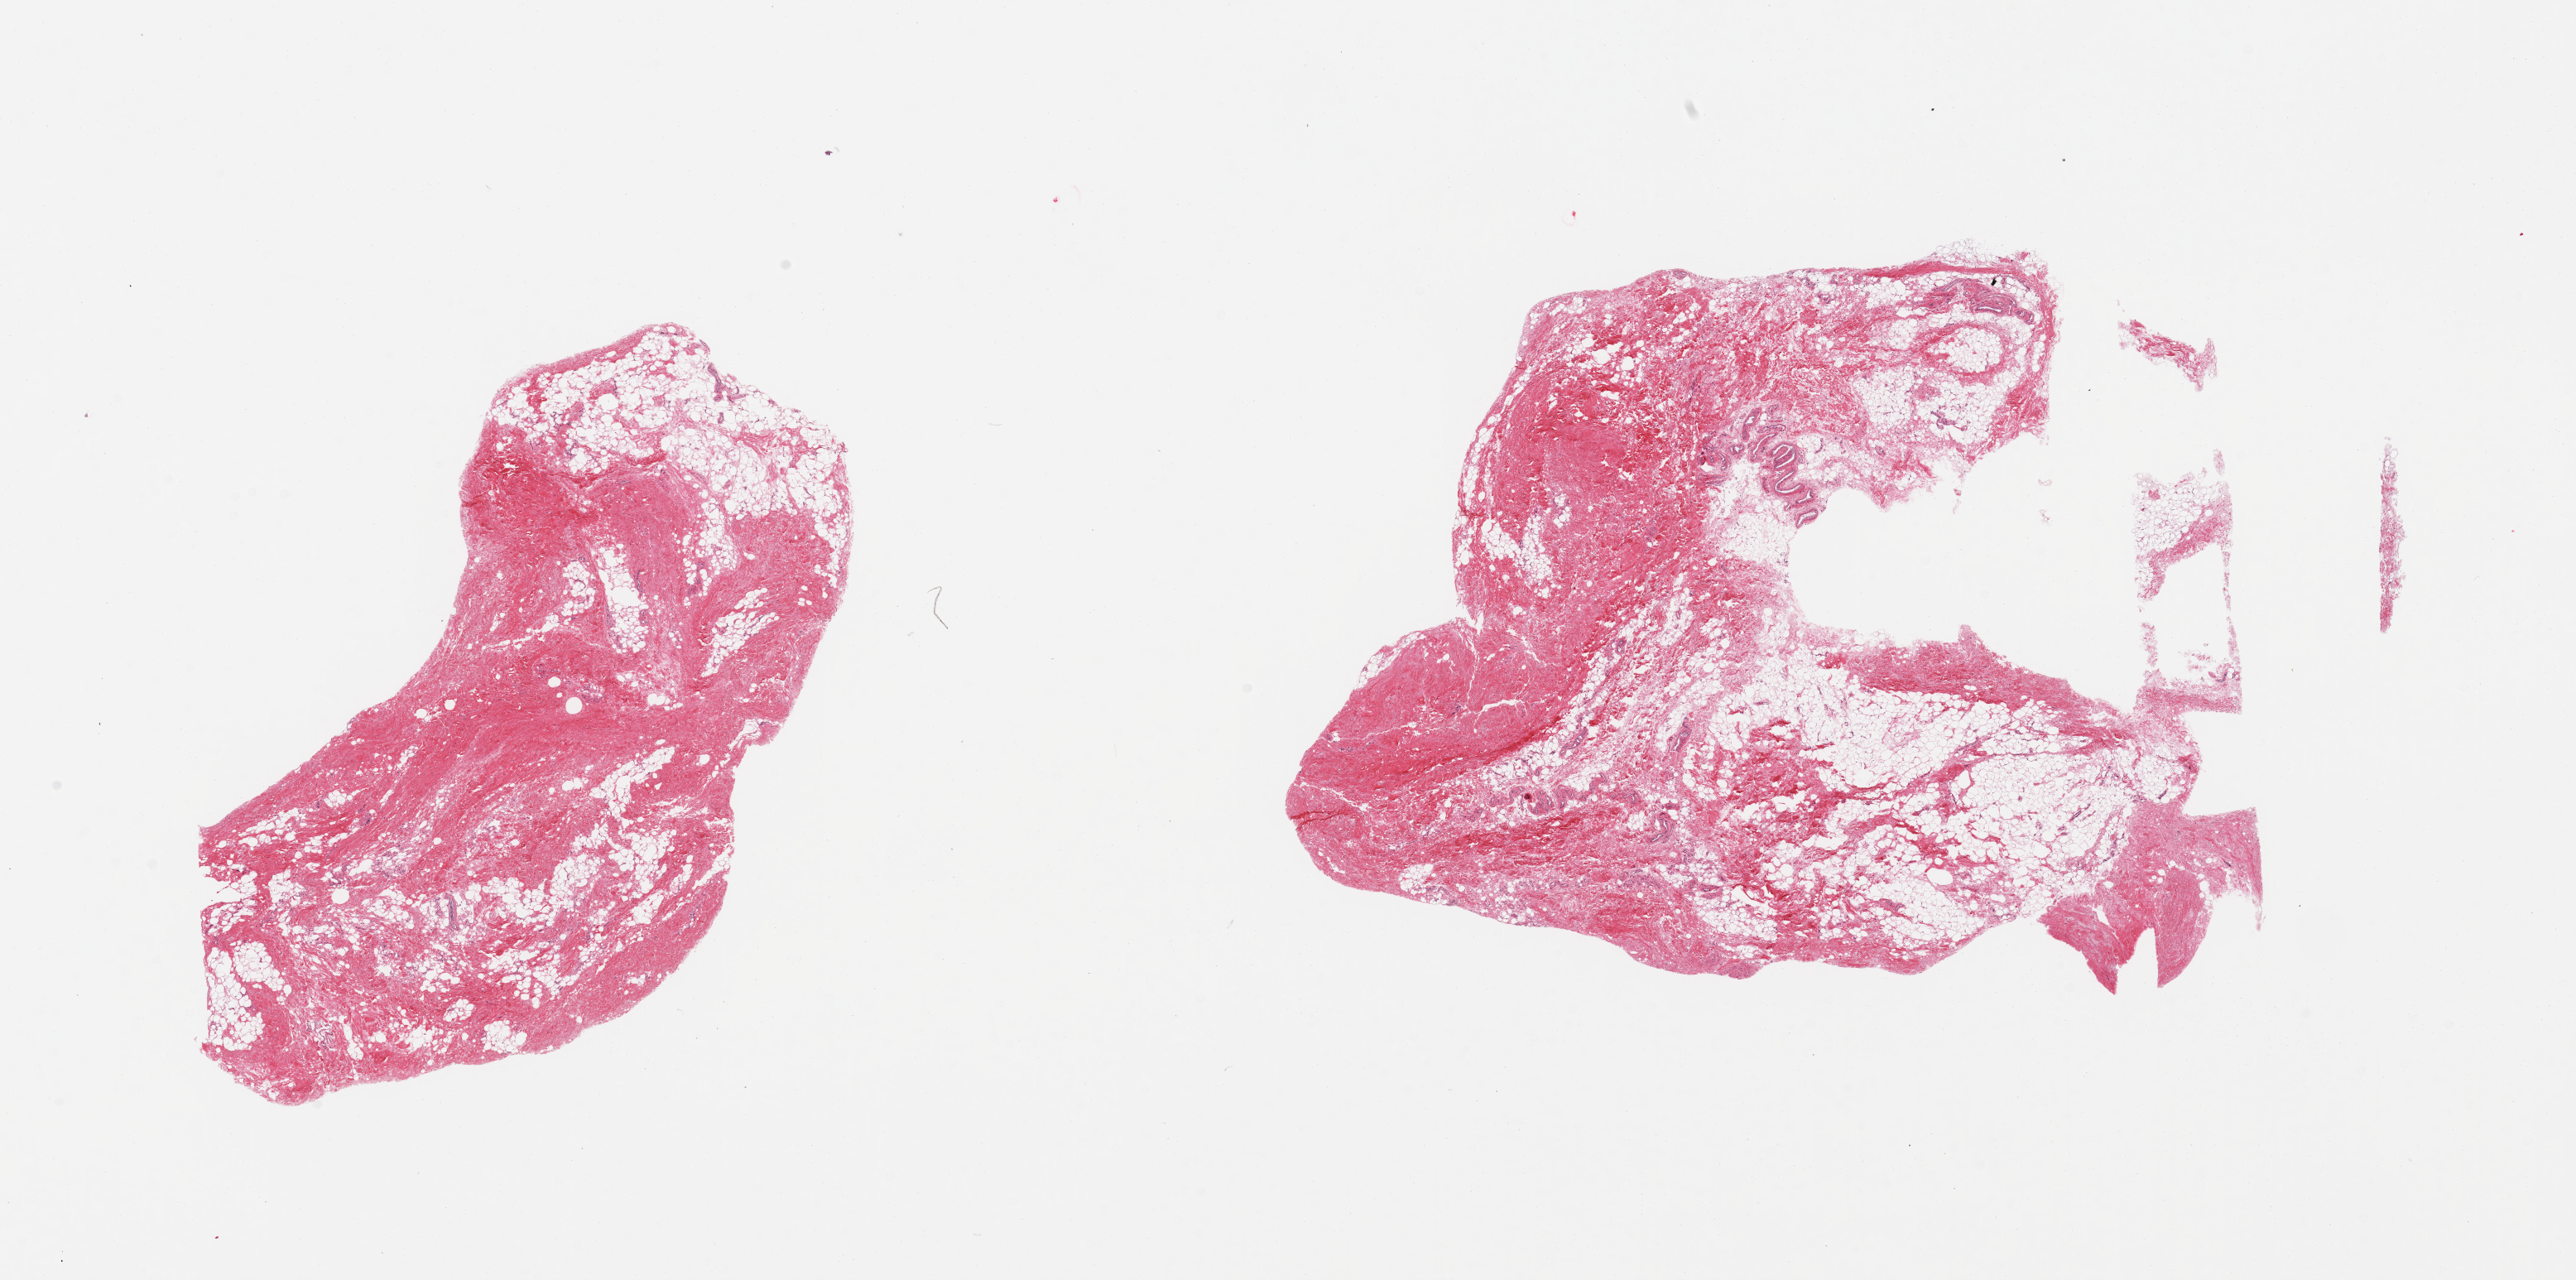
Haematoxylin and eosin whole-slide image — shown as a low-resolution overview of the whole scanned area (about 24.6 x 12.2 mm); PAXgene-fixed, paraffin-embedded tissue; sampled site (target tissue): breast; donor tissue sample. Donor sex: male.
Reviewer comment on this tissue sample: 2 pieces, fibroadipose elements only; gynecomastoid stromal hyperplasia.